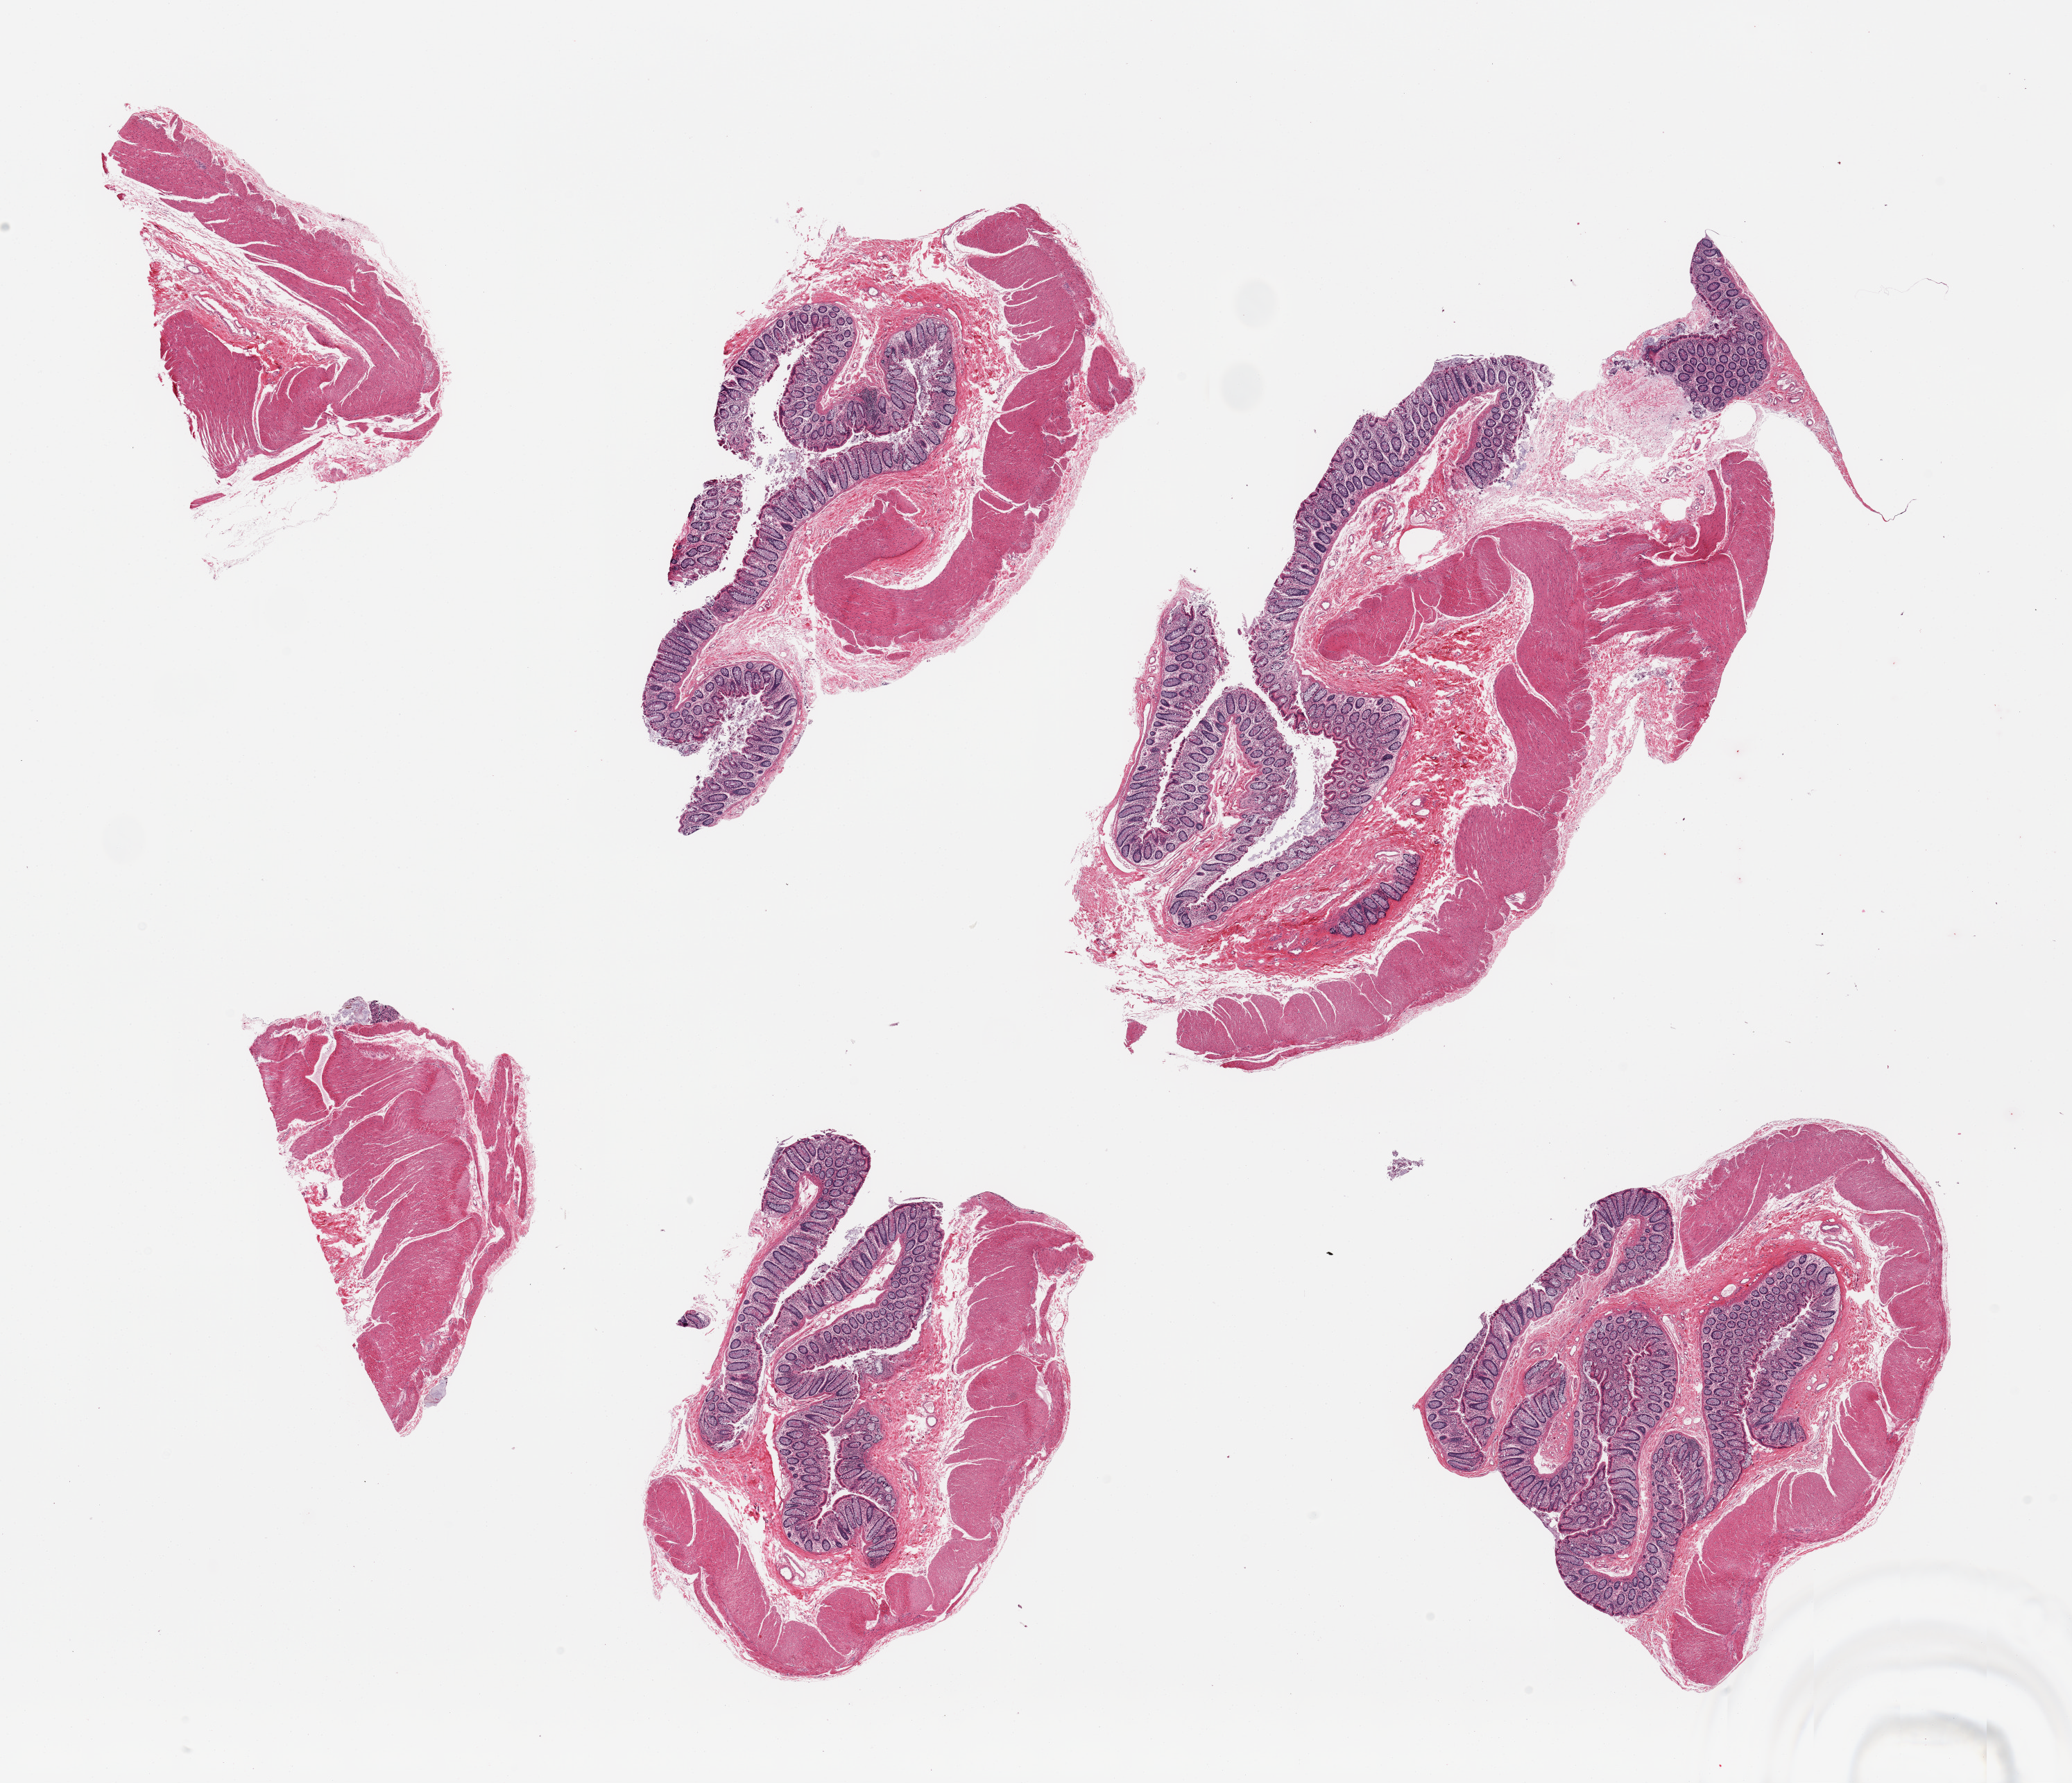
Whole-slide image, H&E stain — shown as a low-resolution overview of the whole scanned area (about 23.6 x 20.3 mm, from a 20x scan); PAXgene-fixed paraffin-embedded (PFPE) section; sampled site (target tissue): transverse colon; tissue donor sample. Donor: male.
* review note (as recorded): 6 pieces; mucosa and muscularis